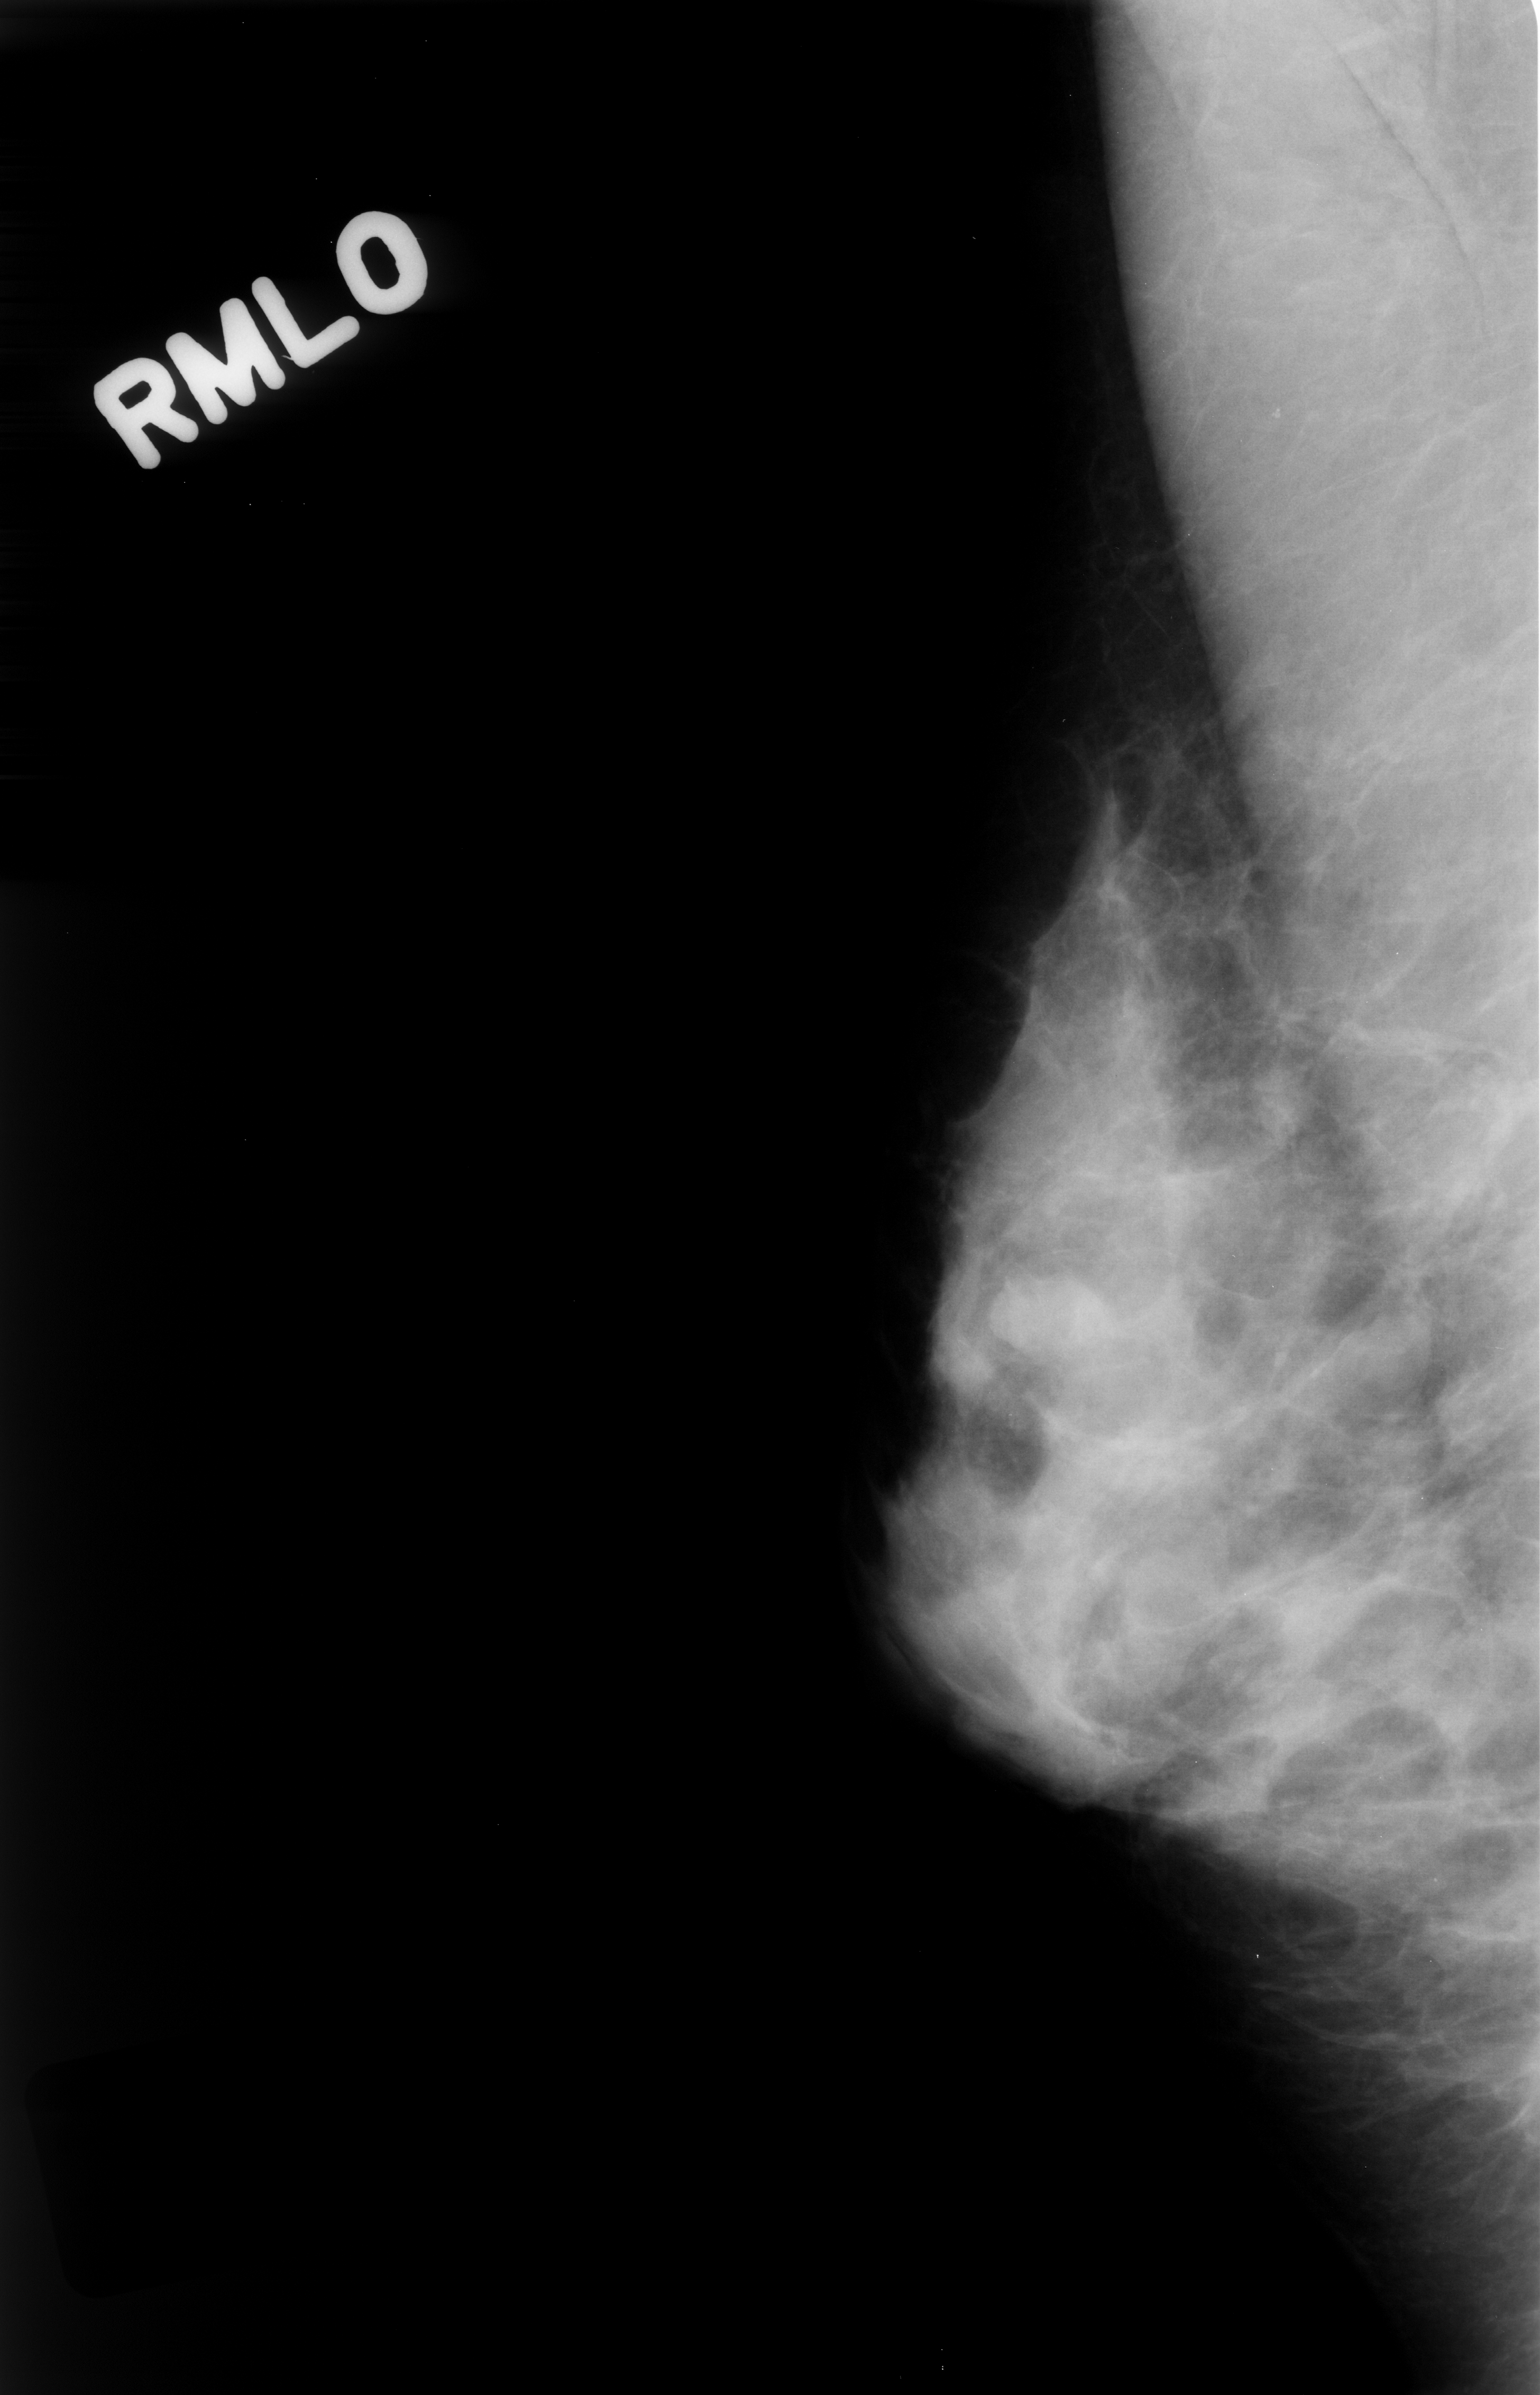
Digitized screen-film mammogram; right breast; mediolateral oblique (MLO) view; breast composition: heterogeneously dense (BI-RADS density category 3 of 4); 1540 × 2395 image matrix.
Expert-marked regions of interest on this image (one box per marked abnormality):
- mass, shape oval, margins circumscribed; BI-RADS assessment category 4; subtlety rating 5 on a 1 (subtle) to 5 (obvious) scale; pathology result (as recorded, not read from the image): benign: bounding box <986,1265,1108,1366> (left, top, right, bottom; pixels)